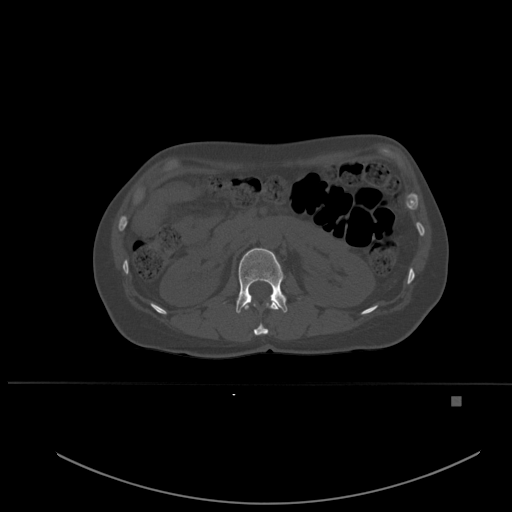
CT including the spine, one axial slice; slice 239 of 651 in the series (ordered by position); bone window (W 1800 / L 400 HU); 1.5 mm slice thickness; 512 × 512 image matrix, field of view 443 × 443 mm. Female patient, age 49 years. Case-level facts recorded for this patient, not image findings: primary cancer: breast; vertebrae with lytic lesions (as recorded): L3, T12, L4.
Structures marked on this image (semi-automatic segmentation, software-assisted and operator-edited):
- L1 vertebra: box from (x=236, y=248) to (x=288, y=313) px
- T12 vertebra: (x=244, y=303)–(x=279, y=335)